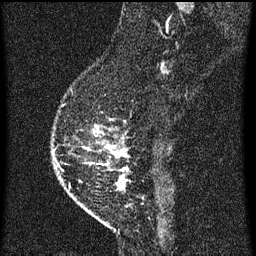
Breast MRI (dynamic contrast-enhanced), one sagittal slice. Slice 17 of 60 in the series (ordered by position). Dynamic contrast-enhanced series, image 2 of 3 at this slice position (ordered by acquisition). 1.5 T. TE 4.2 ms, TR 8 ms. 2 mm slice thickness. 256 × 256 image matrix. Patient: female, 47 years.
Outlined on this slice (semi-automatic segmentation, software-assisted and operator-edited):
- analysis volume of interest (the breast-tissue region the enhancement analysis was run in; not a lesion): bounding box (x1, y1, x2, y2) in pixels: (52, 92, 134, 203)
- tumour enhancement mask (voxels above the 70 % enhancement threshold inside the analysis volume of interest): (53, 126, 125, 187)